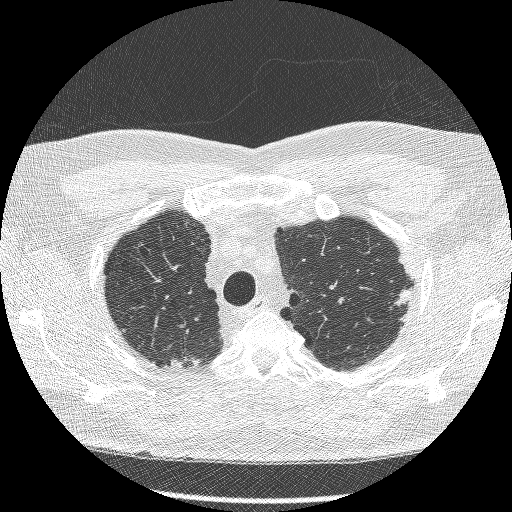
Chest CT (low-dose screening protocol), one axial image. Second annual screen. Lung window (W 1500 / L -600 HU). Lung (sharp) reconstruction kernel (BONE). Slice 226 of 269 in the series. Male, age 66 years at enrolment.
Expert reader's lesion annotation, bounding box (x1, y1, x2, y2) in pixels: (382, 267, 425, 318). Screening reader's record for this exam (one nodule recorded; not confirmed to be the boxed lesion): non-calcified nodule or mass ≥4 mm, right lower lobe, 40 × 19 mm, spiculated (stellate) margins, soft tissue attenuation, pre-existing on the prior screen: yes; interval growth: no. Note: the box lies in the patient's left hemithorax on this image, whereas the reader's record names the right lung; they may be different findings. Participant outcome: lung cancer diagnosed 554 days after this screen (after the third annual screen) — adenocarcinoma, NOS, left upper lobe, poorly differentiated (G3), stage IB (AJCC 6th edition), 16 mm at pathology.